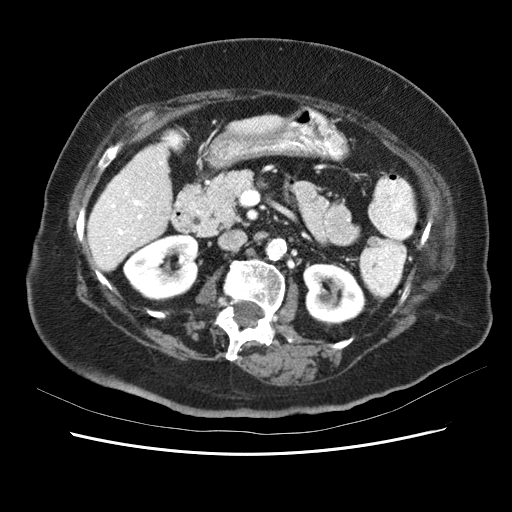
Contrast-enhanced abdominal CT (liver protocol), one axial slice. Reconstruction kernel STANDARD. 120 kVp. Soft-tissue window (W 400 / L 40 HU). 2.5 mm slice thickness. 512 × 512 image matrix, field of view 340 × 340 mm. Case-level facts recorded for this patient, not image findings: diagnosis: hepatocellular carcinoma (patient treated with transarterial chemoembolisation; whether this scan precedes or follows treatment is not stated here); TNM stage (as recorded): Stage-I; Child-Pugh class: B; tumour nodularity: uninodular; tumour size: 5.3 cm.
Structures marked on this image (semi-automatic segmentation, software-assisted and operator-edited):
- liver parenchyma outside the tumour (the mass and vessels are separate outlines, so this box may not span the whole liver): box from (x=88, y=134) to (x=176, y=274) px
- liver vessels: (x=94, y=139)–(x=165, y=269)